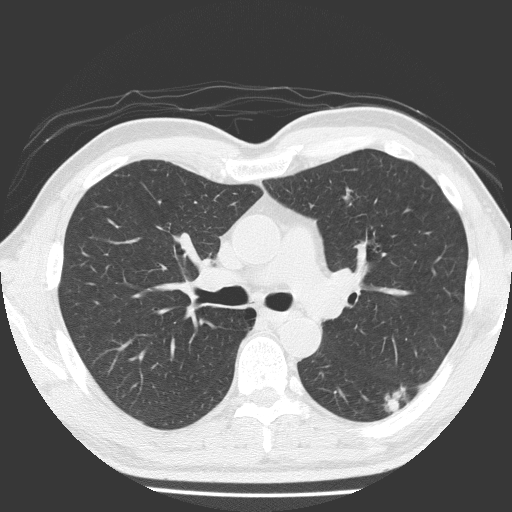
Chest CT (low-dose screening protocol), one axial image, baseline annual screen, lung window (W 1500 / L -600 HU), slice 71 of 184 in the series, 512 × 512 image matrix, field of view 348 × 348 mm. Male, age 58 years at enrolment. Current smoker at enrolment.
• Lesion marked by an expert reader, bounding box (x1, y1, x2, y2) in pixels: (374, 374, 424, 422).
• The screening reader recorded 4 non-calcified nodules or masses ≥4 mm on this exam (left lower lobe, left lower lobe, right middle lobe, left upper lobe); which of them this box marks is not recorded.
• Official screen result: positive, change unspecified: nodule(s) >= 4 mm or enlarging nodule(s), mass(es), or other non-specific abnormalities suspicious for lung cancer.
• Later outcome: lung cancer diagnosed 99 days after this screen — adenosquamous carcinoma, left lower lobe, moderately differentiated (G2), stage IA (AJCC 6th edition), 28 mm at pathology.